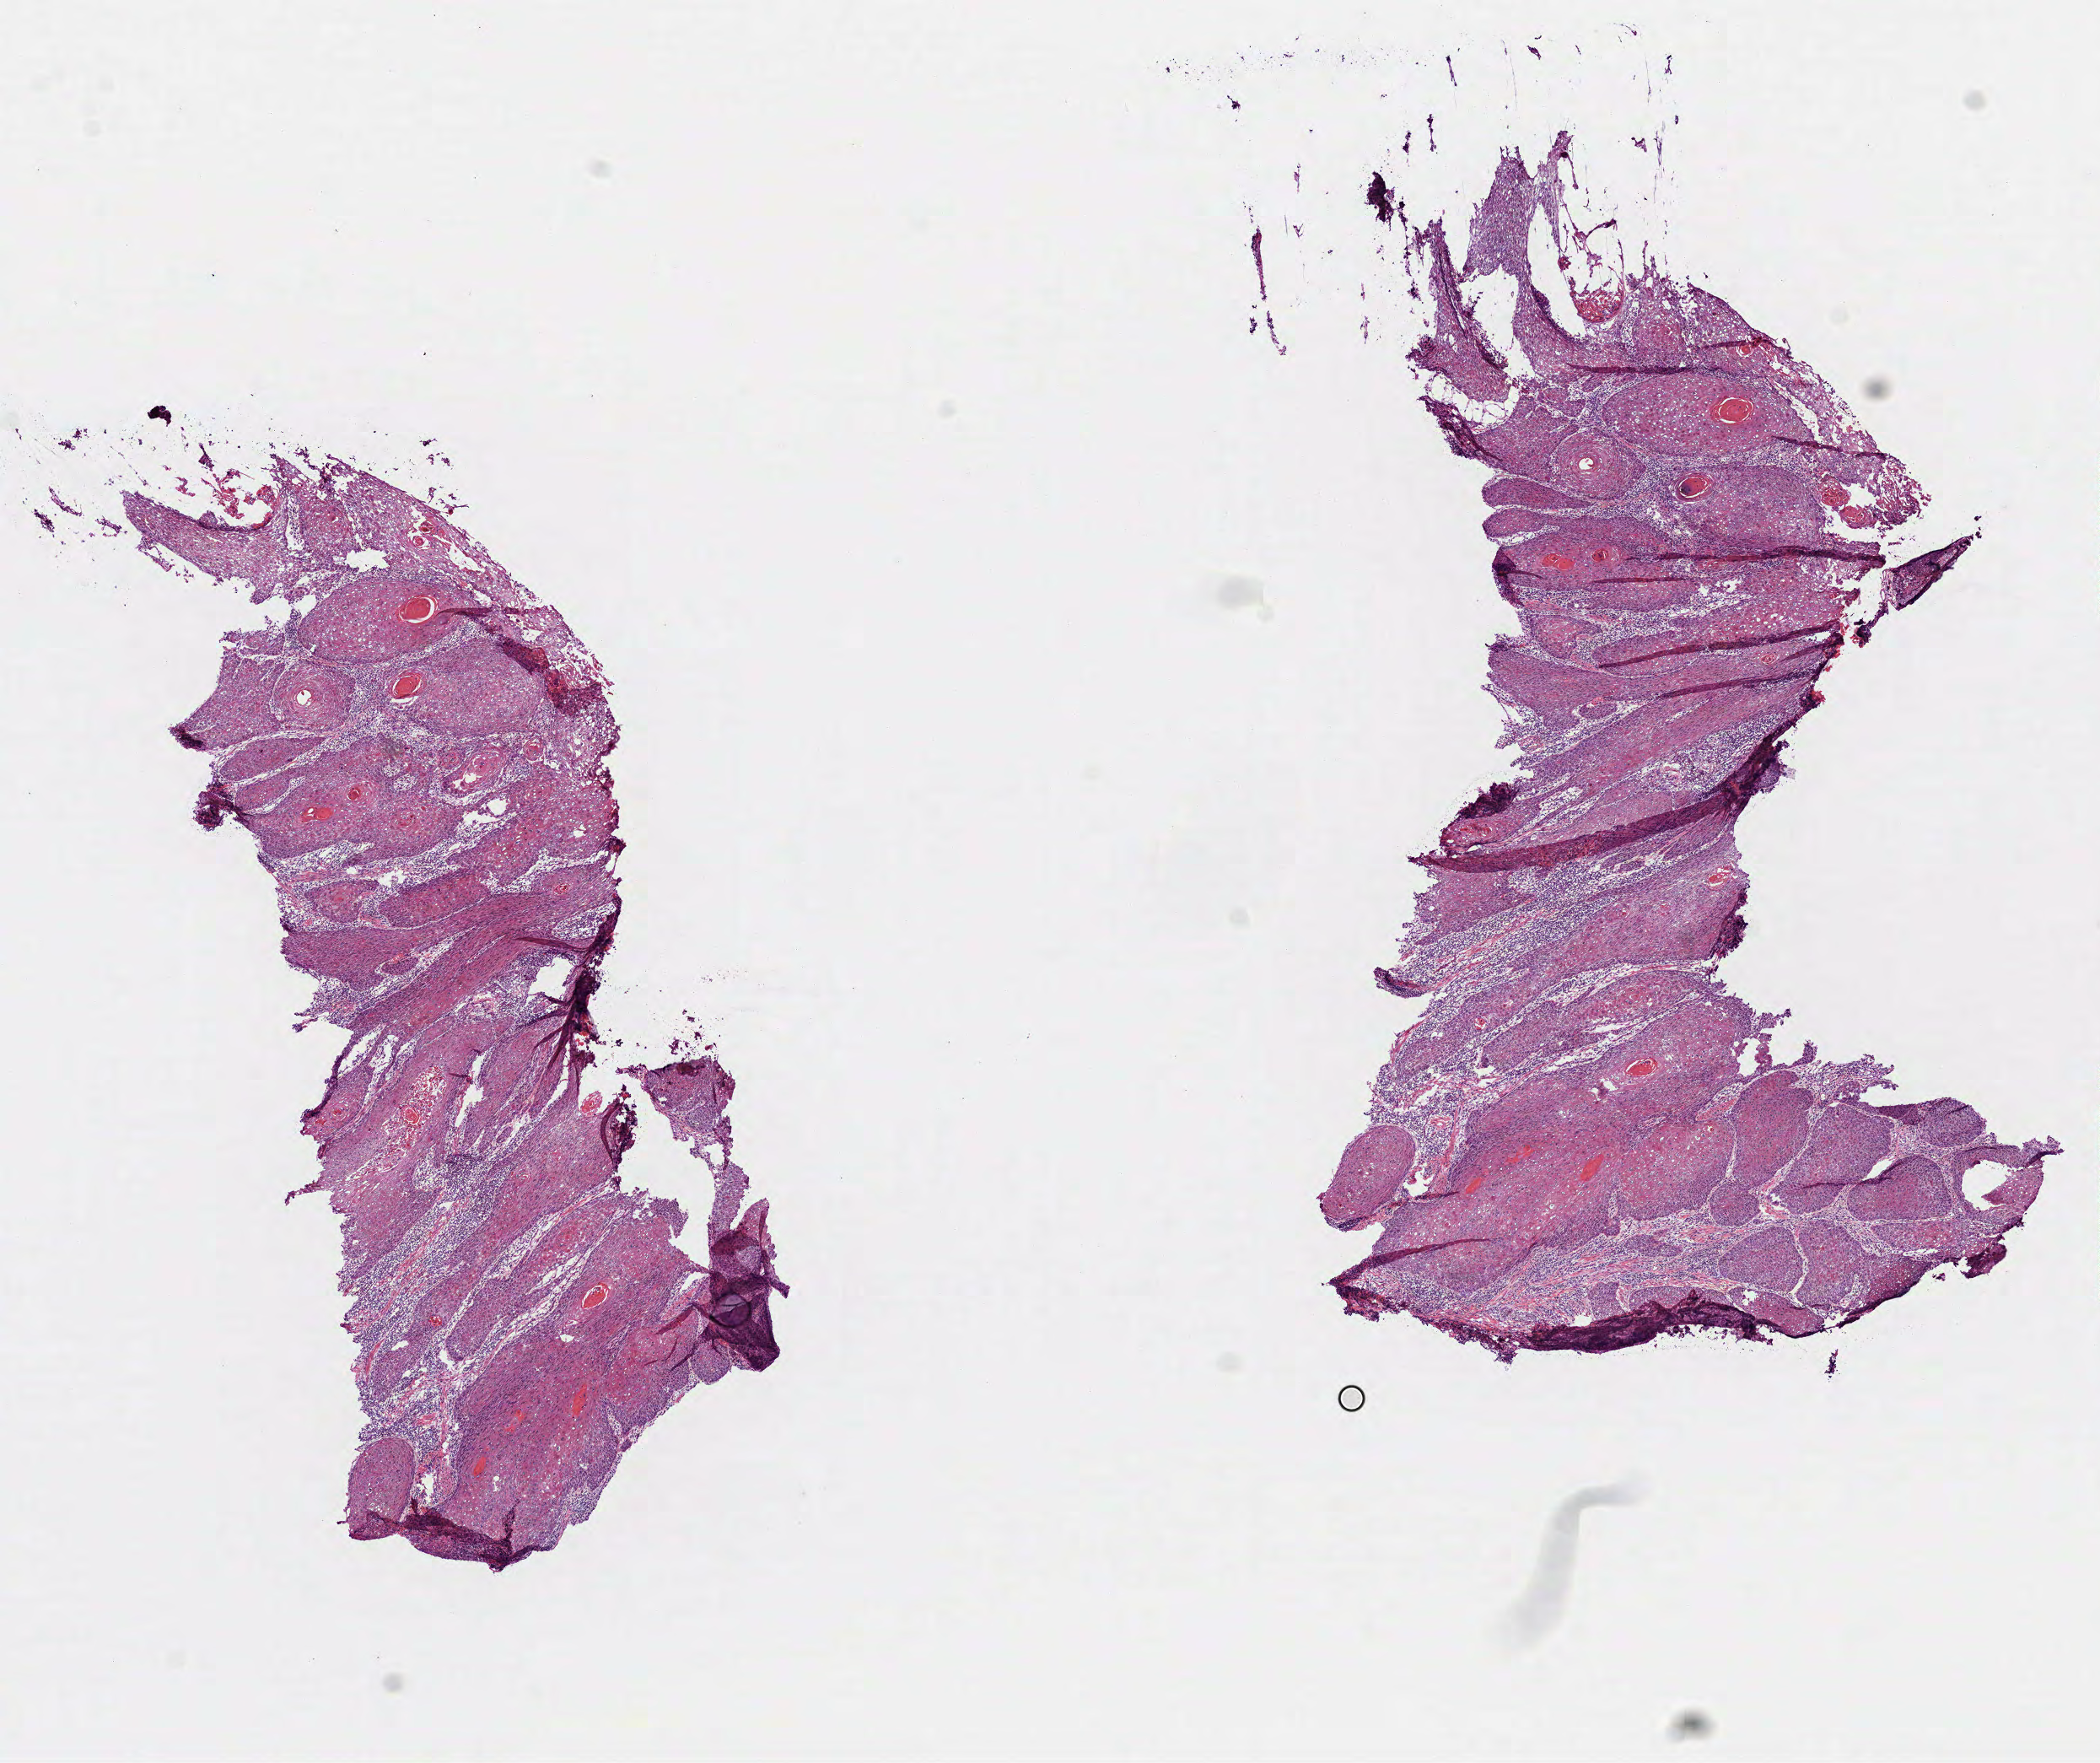
Whole-slide histology image, Hematoxylin and eosin (H&E) stained — a low-resolution overview of the entire scanned area, about 10.0 x 8.4 mm, frozen section, sample: primary tumour, head and neck. Male, age 69 years at initial diagnosis.
Diagnosis: Squamous cell carcinoma, NOS (overlapping lesion of lip, oral cavity and pharynx).